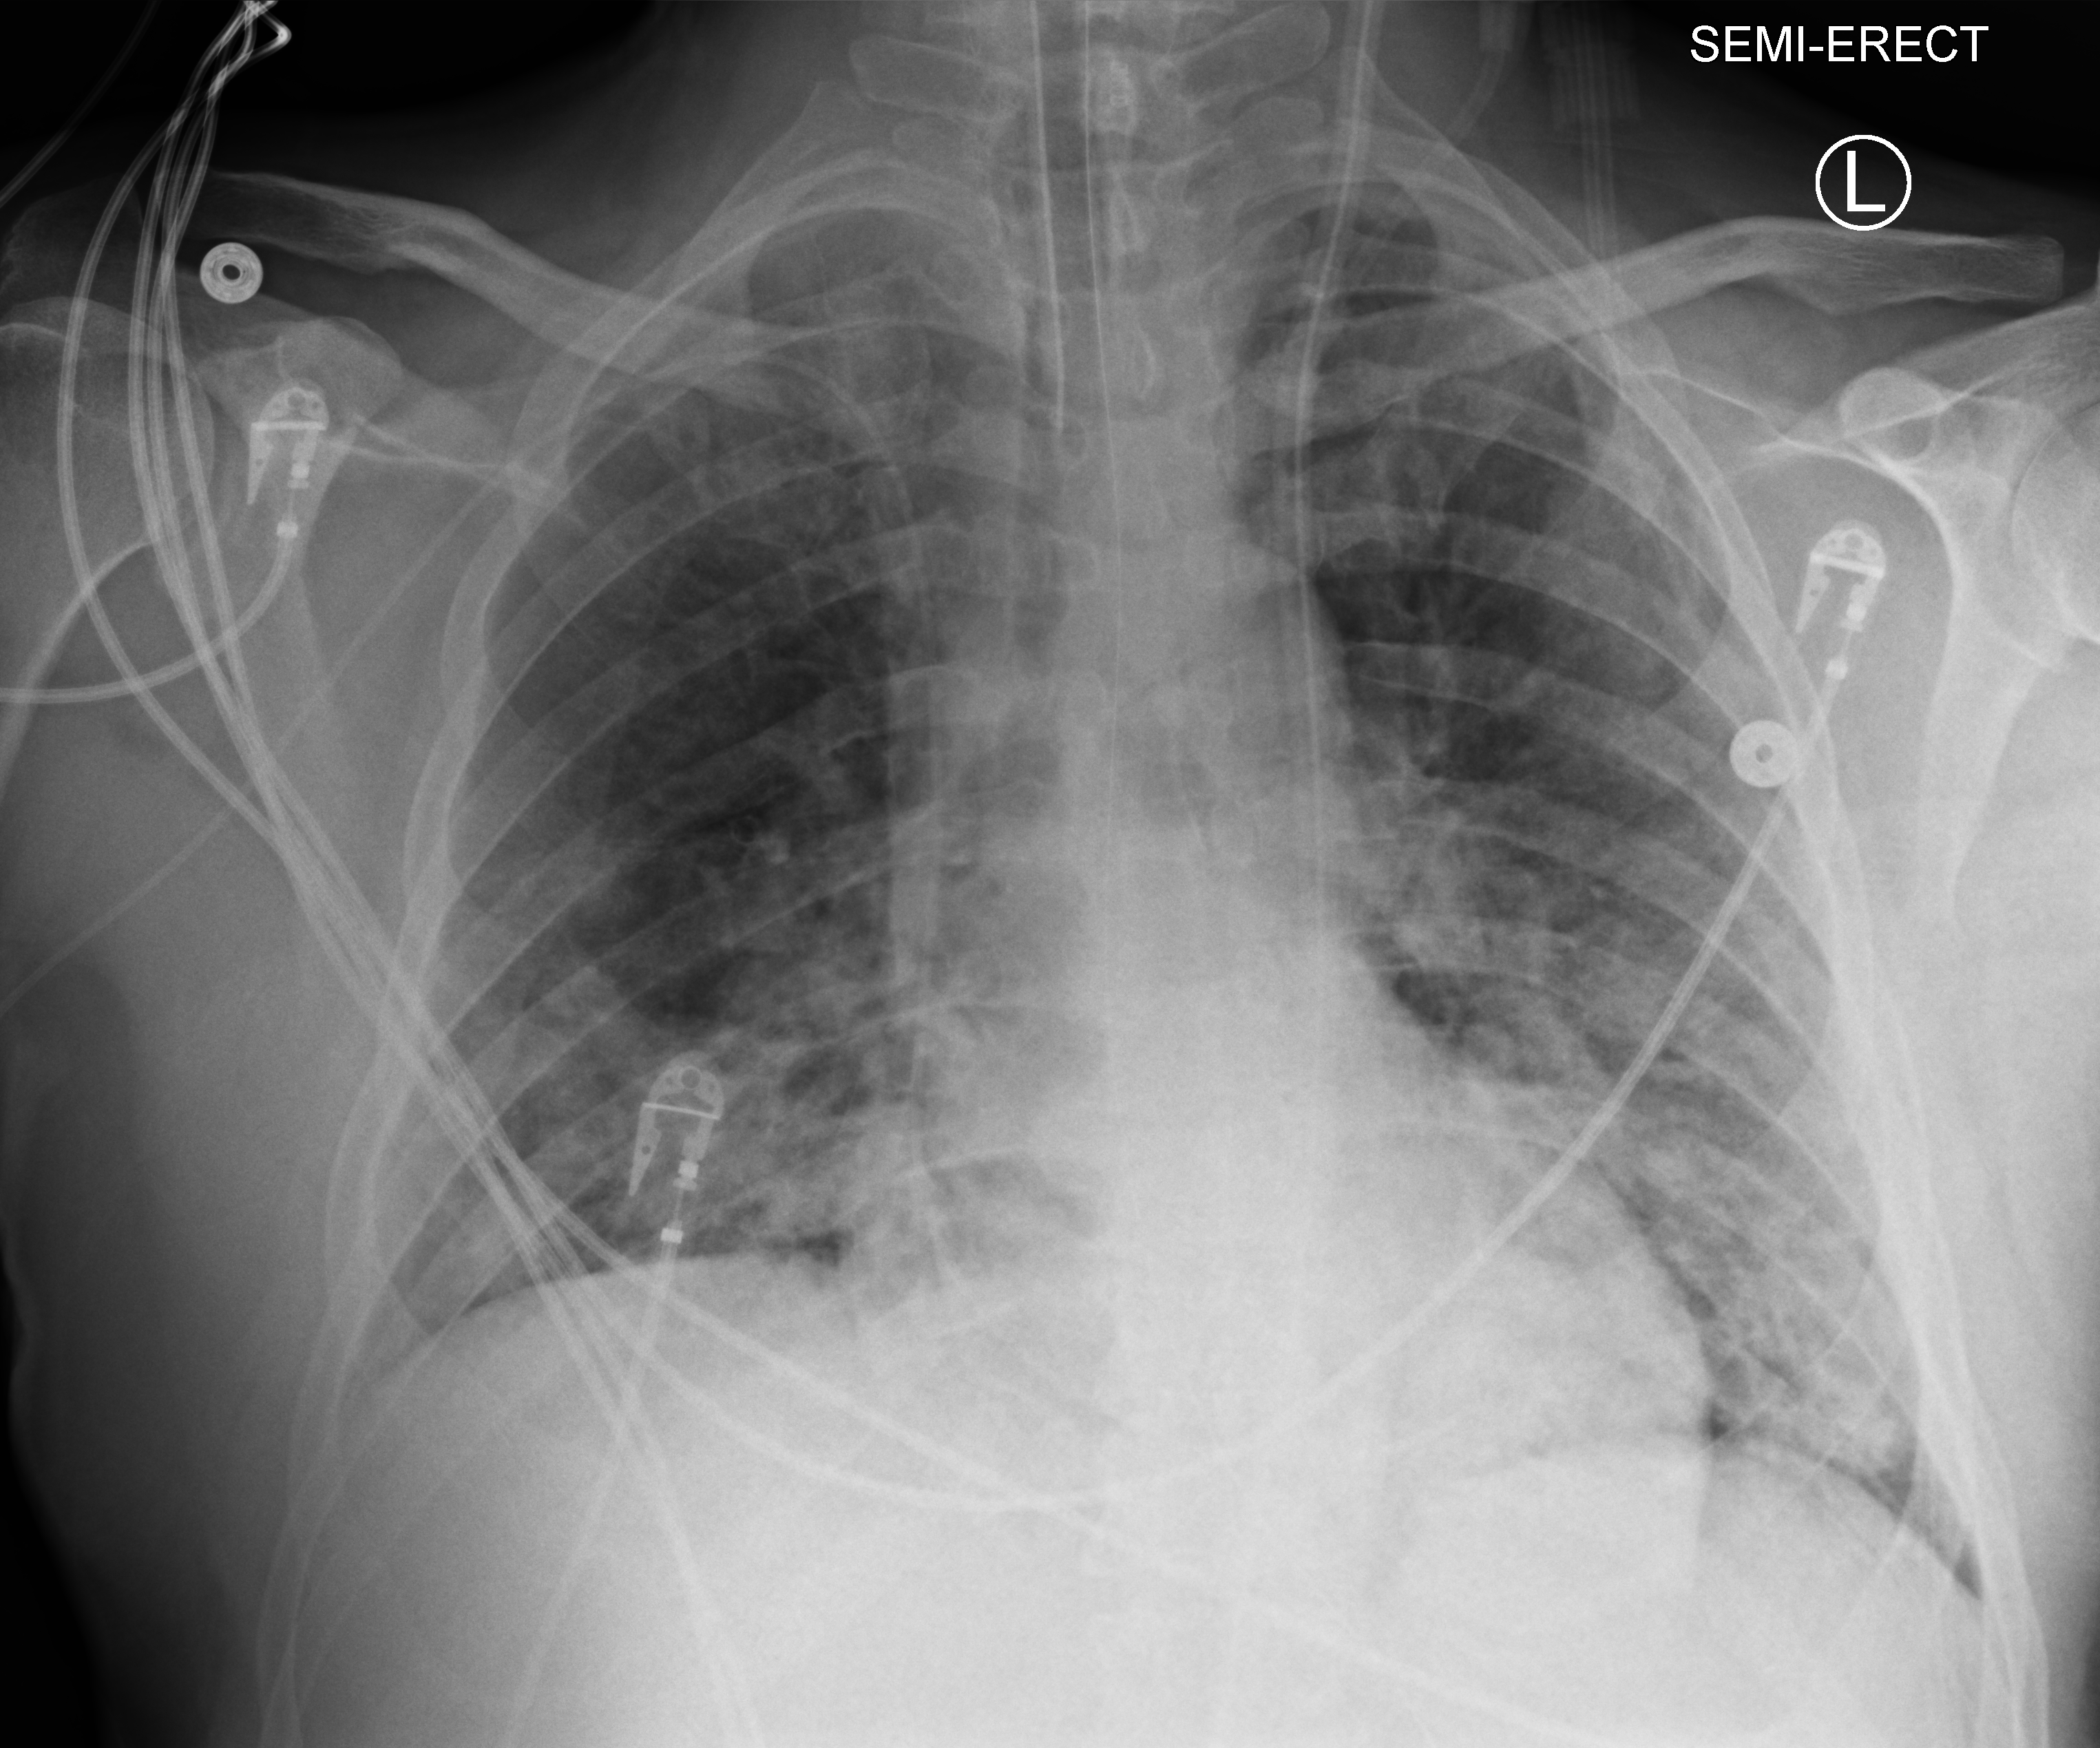
Bedside chest radiograph (computed radiography); anteroposterior (AP) projection. Patient hospitalised with COVID-19; male, aged 18–59 years.
Admission-level facts for this patient (not findings on this image; timing relative to this image not recorded): length of hospital stay: 32 days; admitted to intensive care during this hospital stay: no; mechanically ventilated during this hospital stay: yes.